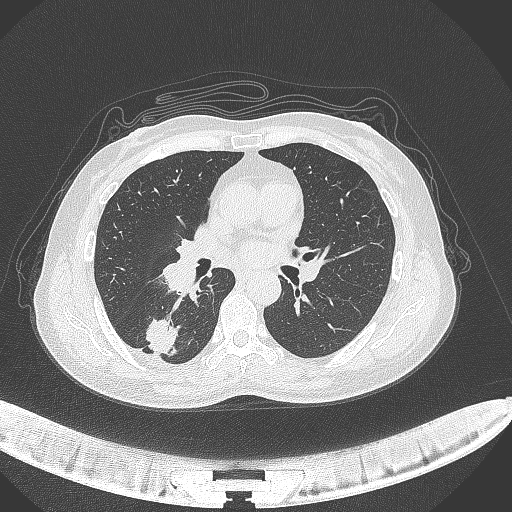
Chest CT, one axial slice. Position 163 of 352 along the scan axis. Lung window (W 1500 / L -600 HU). 1 mm slice thickness. 512 × 512 image matrix, field of view 400 × 400 mm. Female patient, age 55 years. From the clinical record (not read from this slice): clinical TNM (as recorded): T1c N1 M0.
Annotated regions visible in this slice (bounding box drawn by a radiologist):
- lung tumour (recorded histology: adenocarcinoma): box from (x=143, y=314) to (x=180, y=358) px